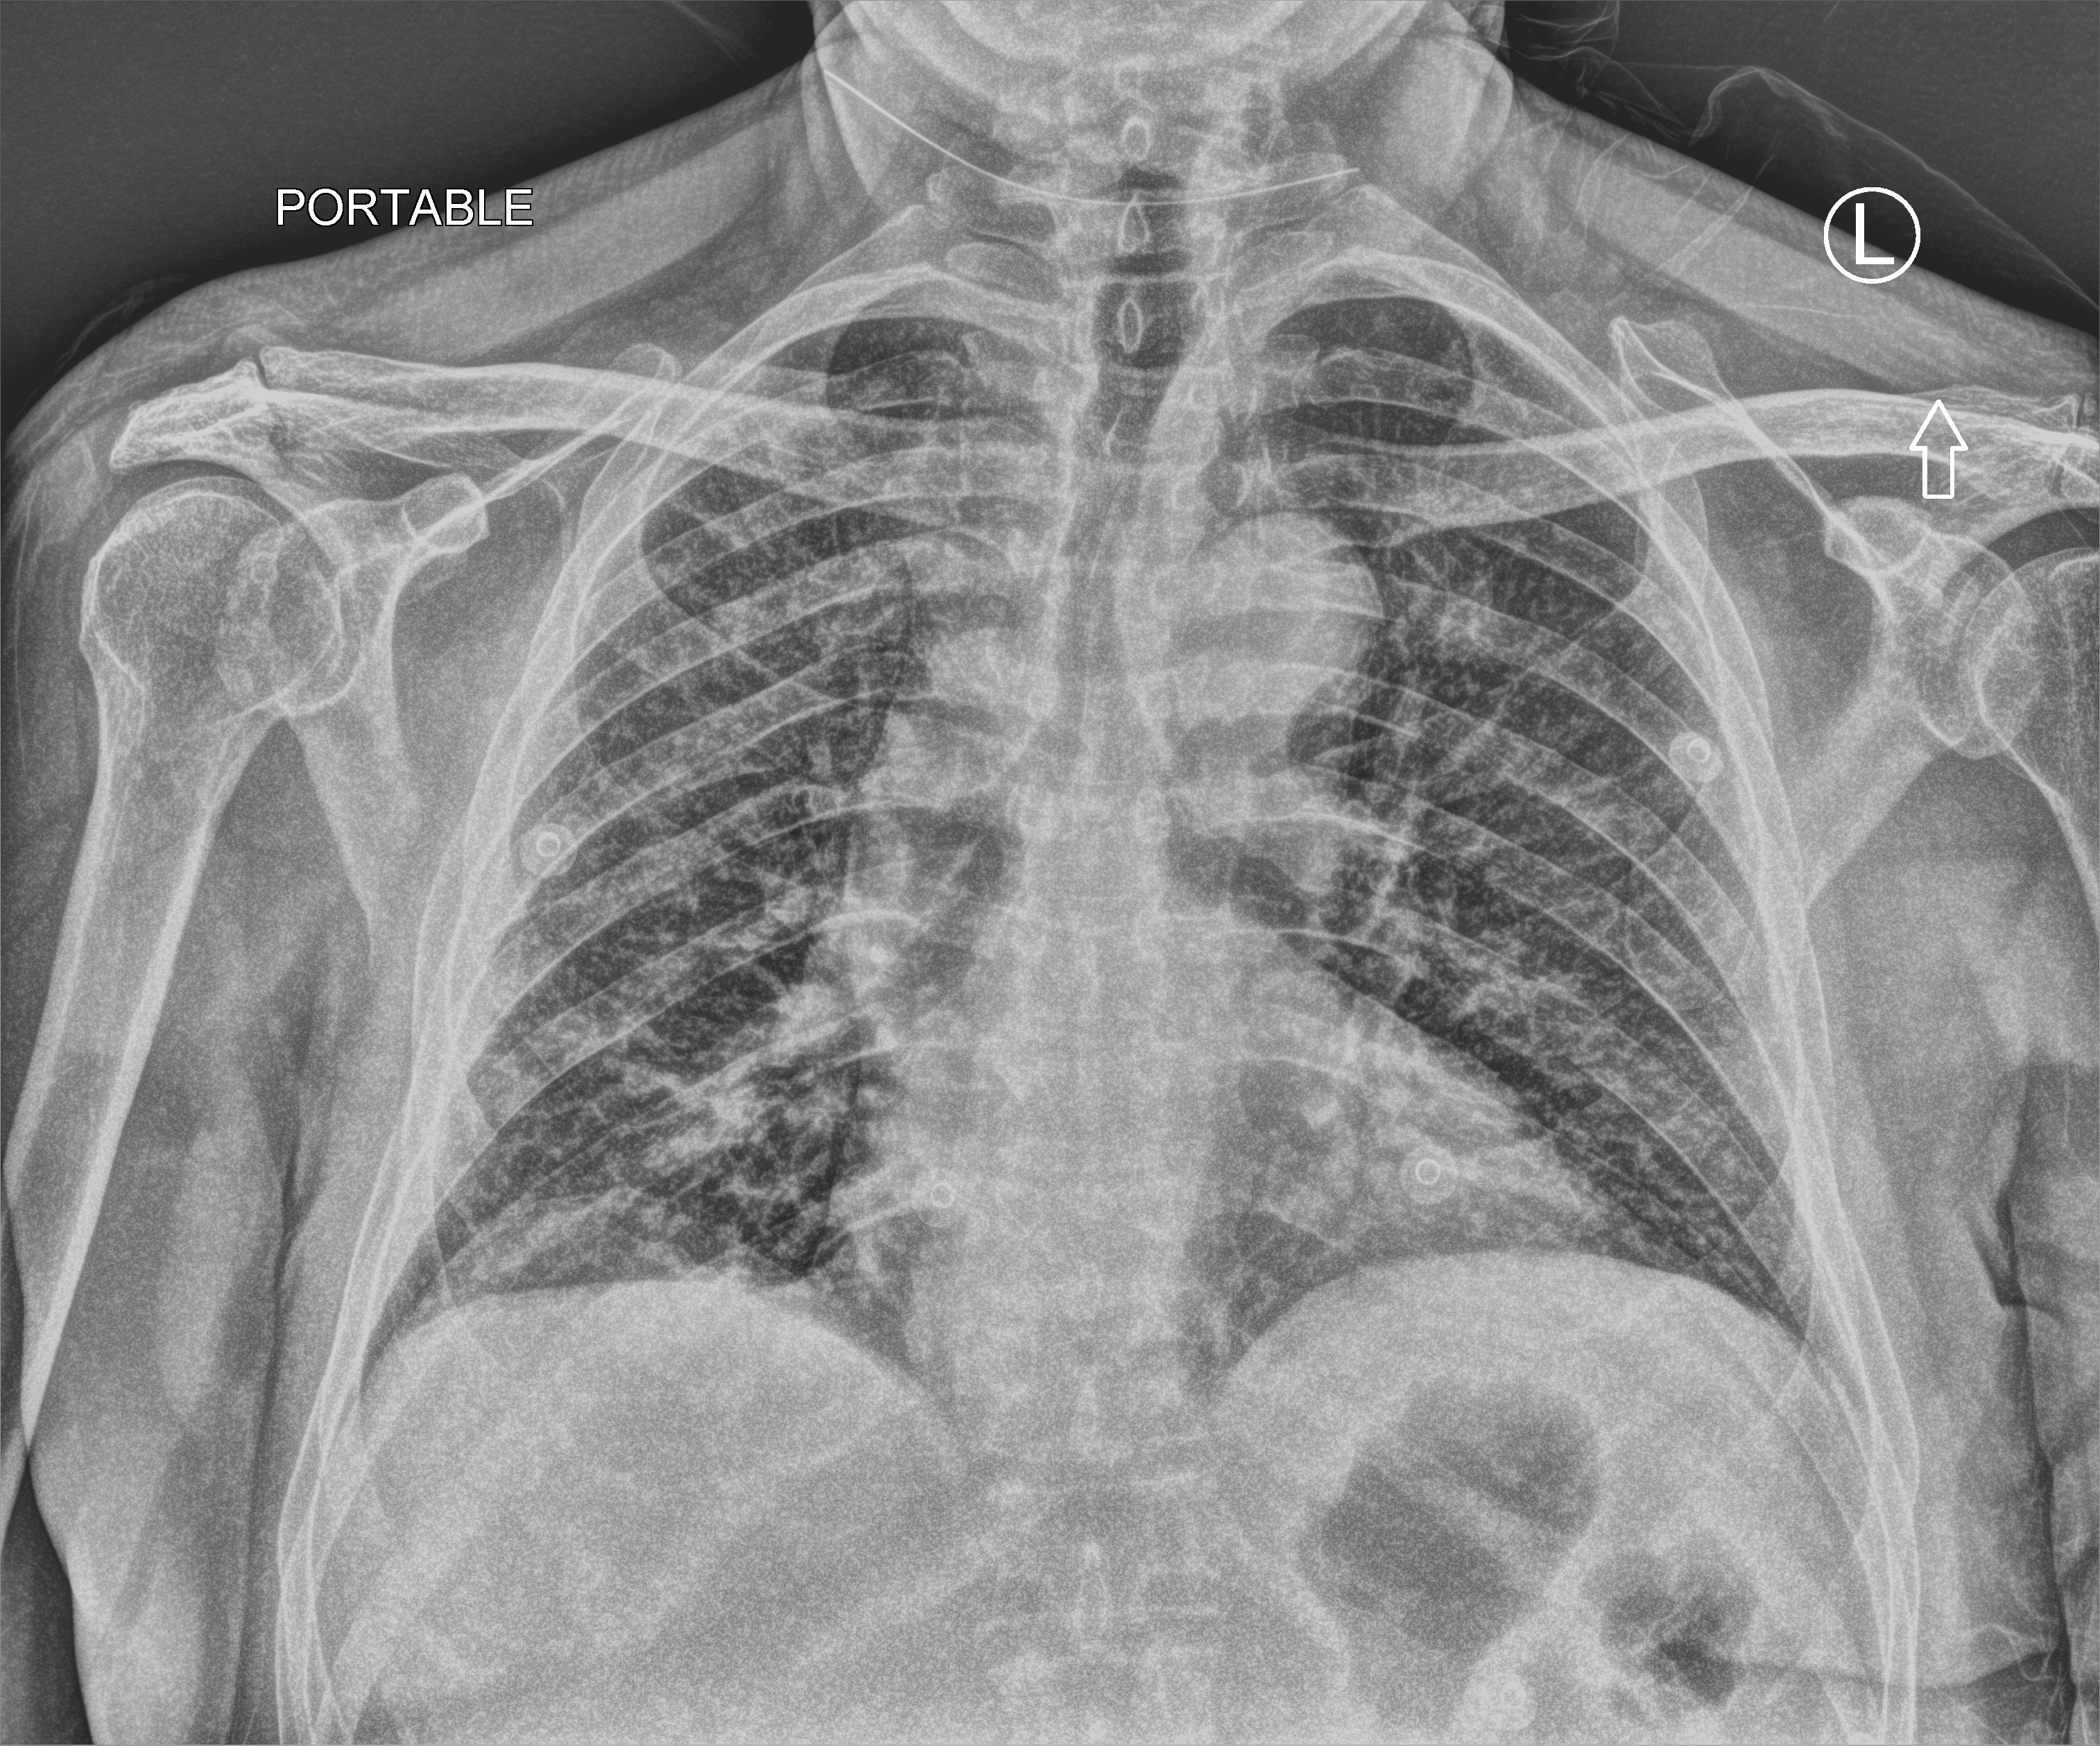
Portable chest radiograph, anteroposterior (AP) projection. Male patient hospitalised with COVID-19, age 60–74 years.
Admission-level facts for this patient (not findings on this image; timing relative to this image not recorded): admitted to intensive care during this hospital stay: no.